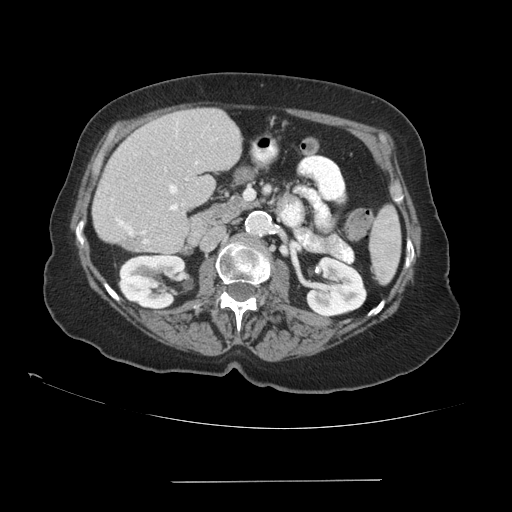
Contrast-enhanced abdominal CT (liver protocol), one axial slice; position 40 of 89 along the scan axis; reconstruction kernel STANDARD; 140 kVp; soft-tissue window (W 400 / L 40 HU); 2.5 mm slice thickness; 512 × 512 image matrix, field of view 400 × 400 mm. From the clinical record (not read from this slice): diagnosis: hepatocellular carcinoma (patient treated with transarterial chemoembolisation; whether this scan precedes or follows treatment is not stated here); TNM stage (as recorded): Stage-IVA; Child-Pugh class: A; tumour differentiation: poorly differentiated; tumour nodularity: uninodular.
Outlined on this slice (semi-automatically segmented with operator editing):
- liver parenchyma outside the tumour (the mass and vessels are separate outlines, so this box may not span the whole liver): box from (x=92, y=108) to (x=242, y=252) px
- liver vessels: (x=116, y=162)–(x=198, y=244)